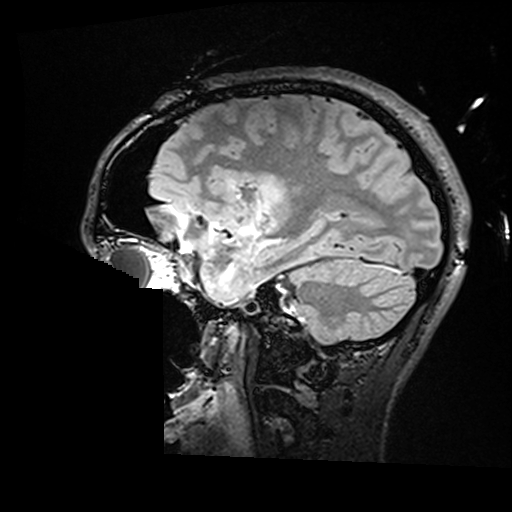
Brain MRI from a brain-tumour surgery series, one sagittal slice; position 111 of 176 along the scan axis; T2 FLAIR; 1 mm slice thickness; 512 × 512 image matrix, field of view 250 × 250 mm. From the clinical record (not read from this slice): histopathology: Astrocytoma; WHO grade: 2; IDH mutation: yes.
Annotated regions visible in this slice (manually delineated by an expert):
- residual tumour: box from (x=260, y=182) to (x=287, y=212) px